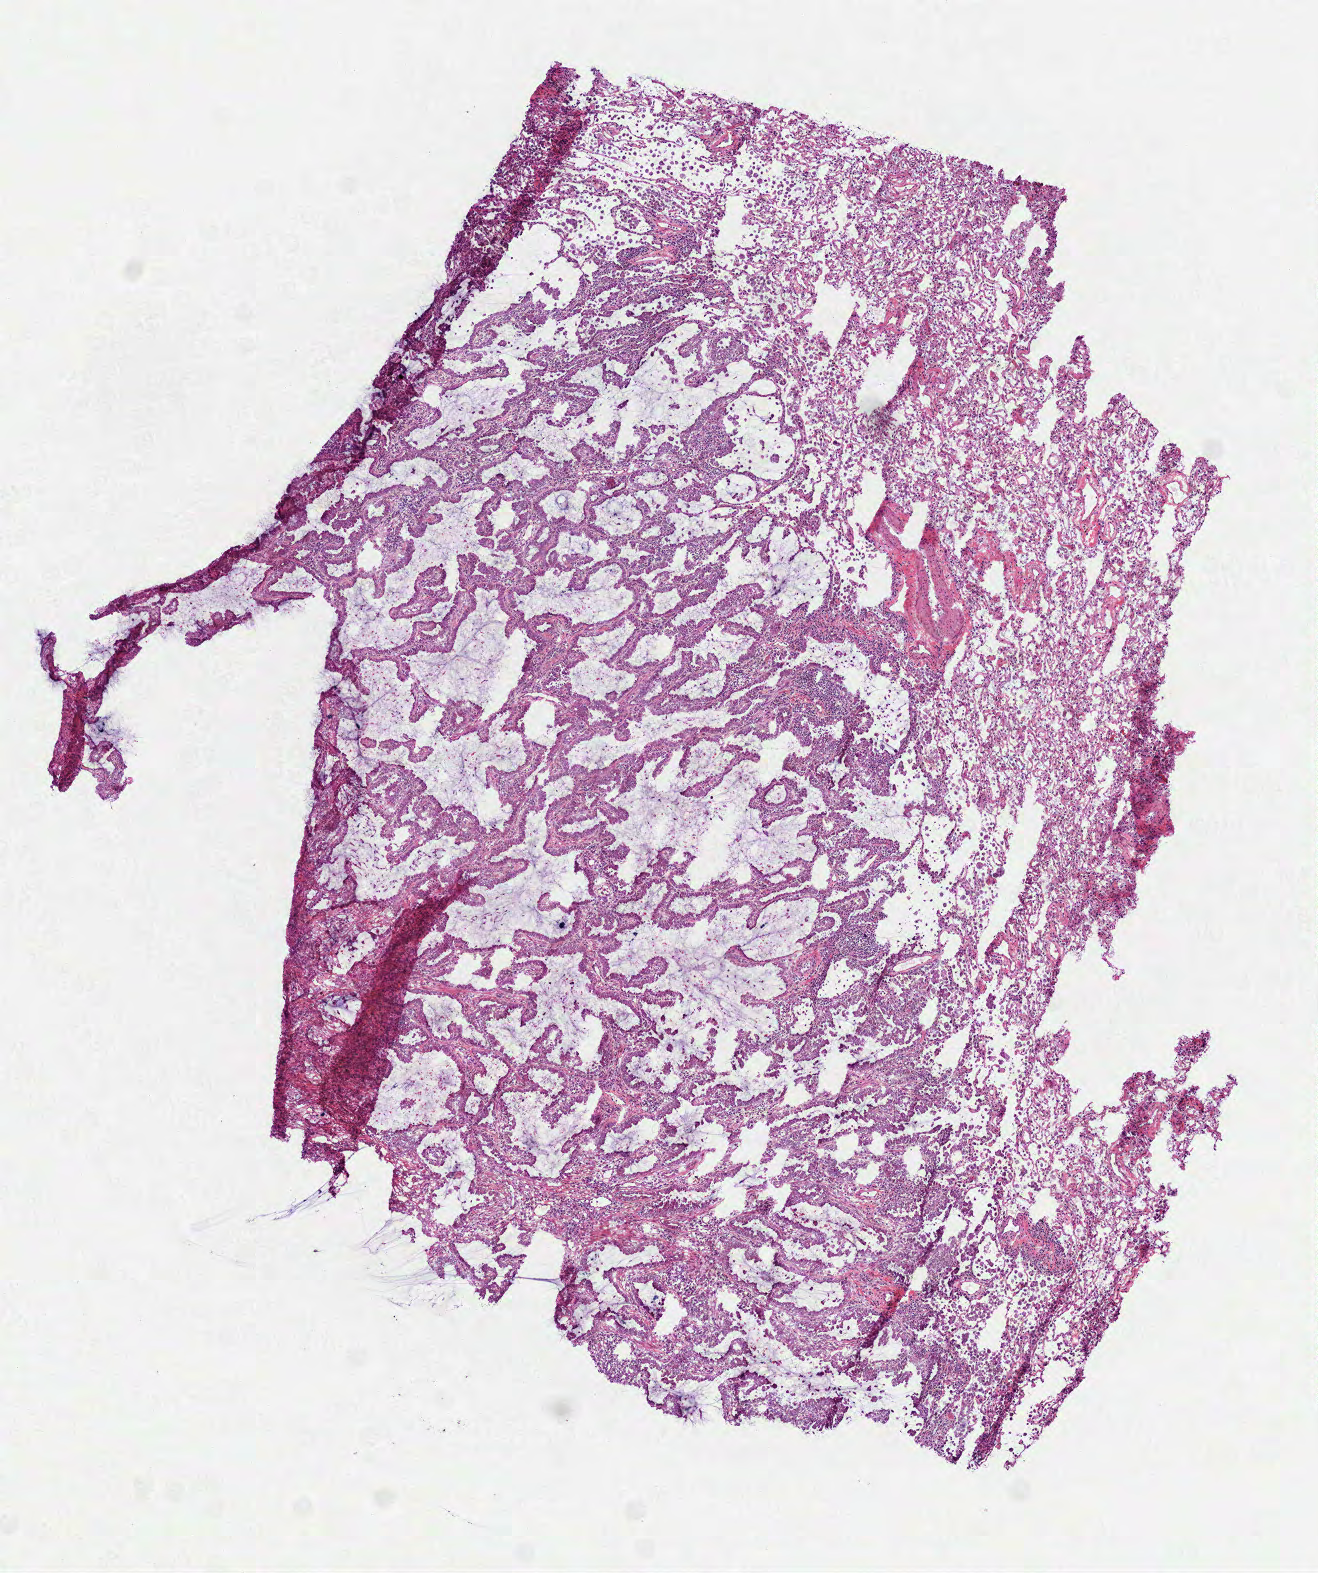
Whole-slide histology image, H&E — whole scanned area (about 5.3 x 6.3 mm, from a 40x scan) shown as a low-resolution overview. Frozen section from the top of the tissue portion. Lung, primary tumour sample. Male, age 69 years at initial diagnosis. Pathologist review of this section (percent, as recorded): tumour cells 75%, tumour nuclei 60%.
Diagnosis: Acinar cell carcinoma (middle lobe, lung).